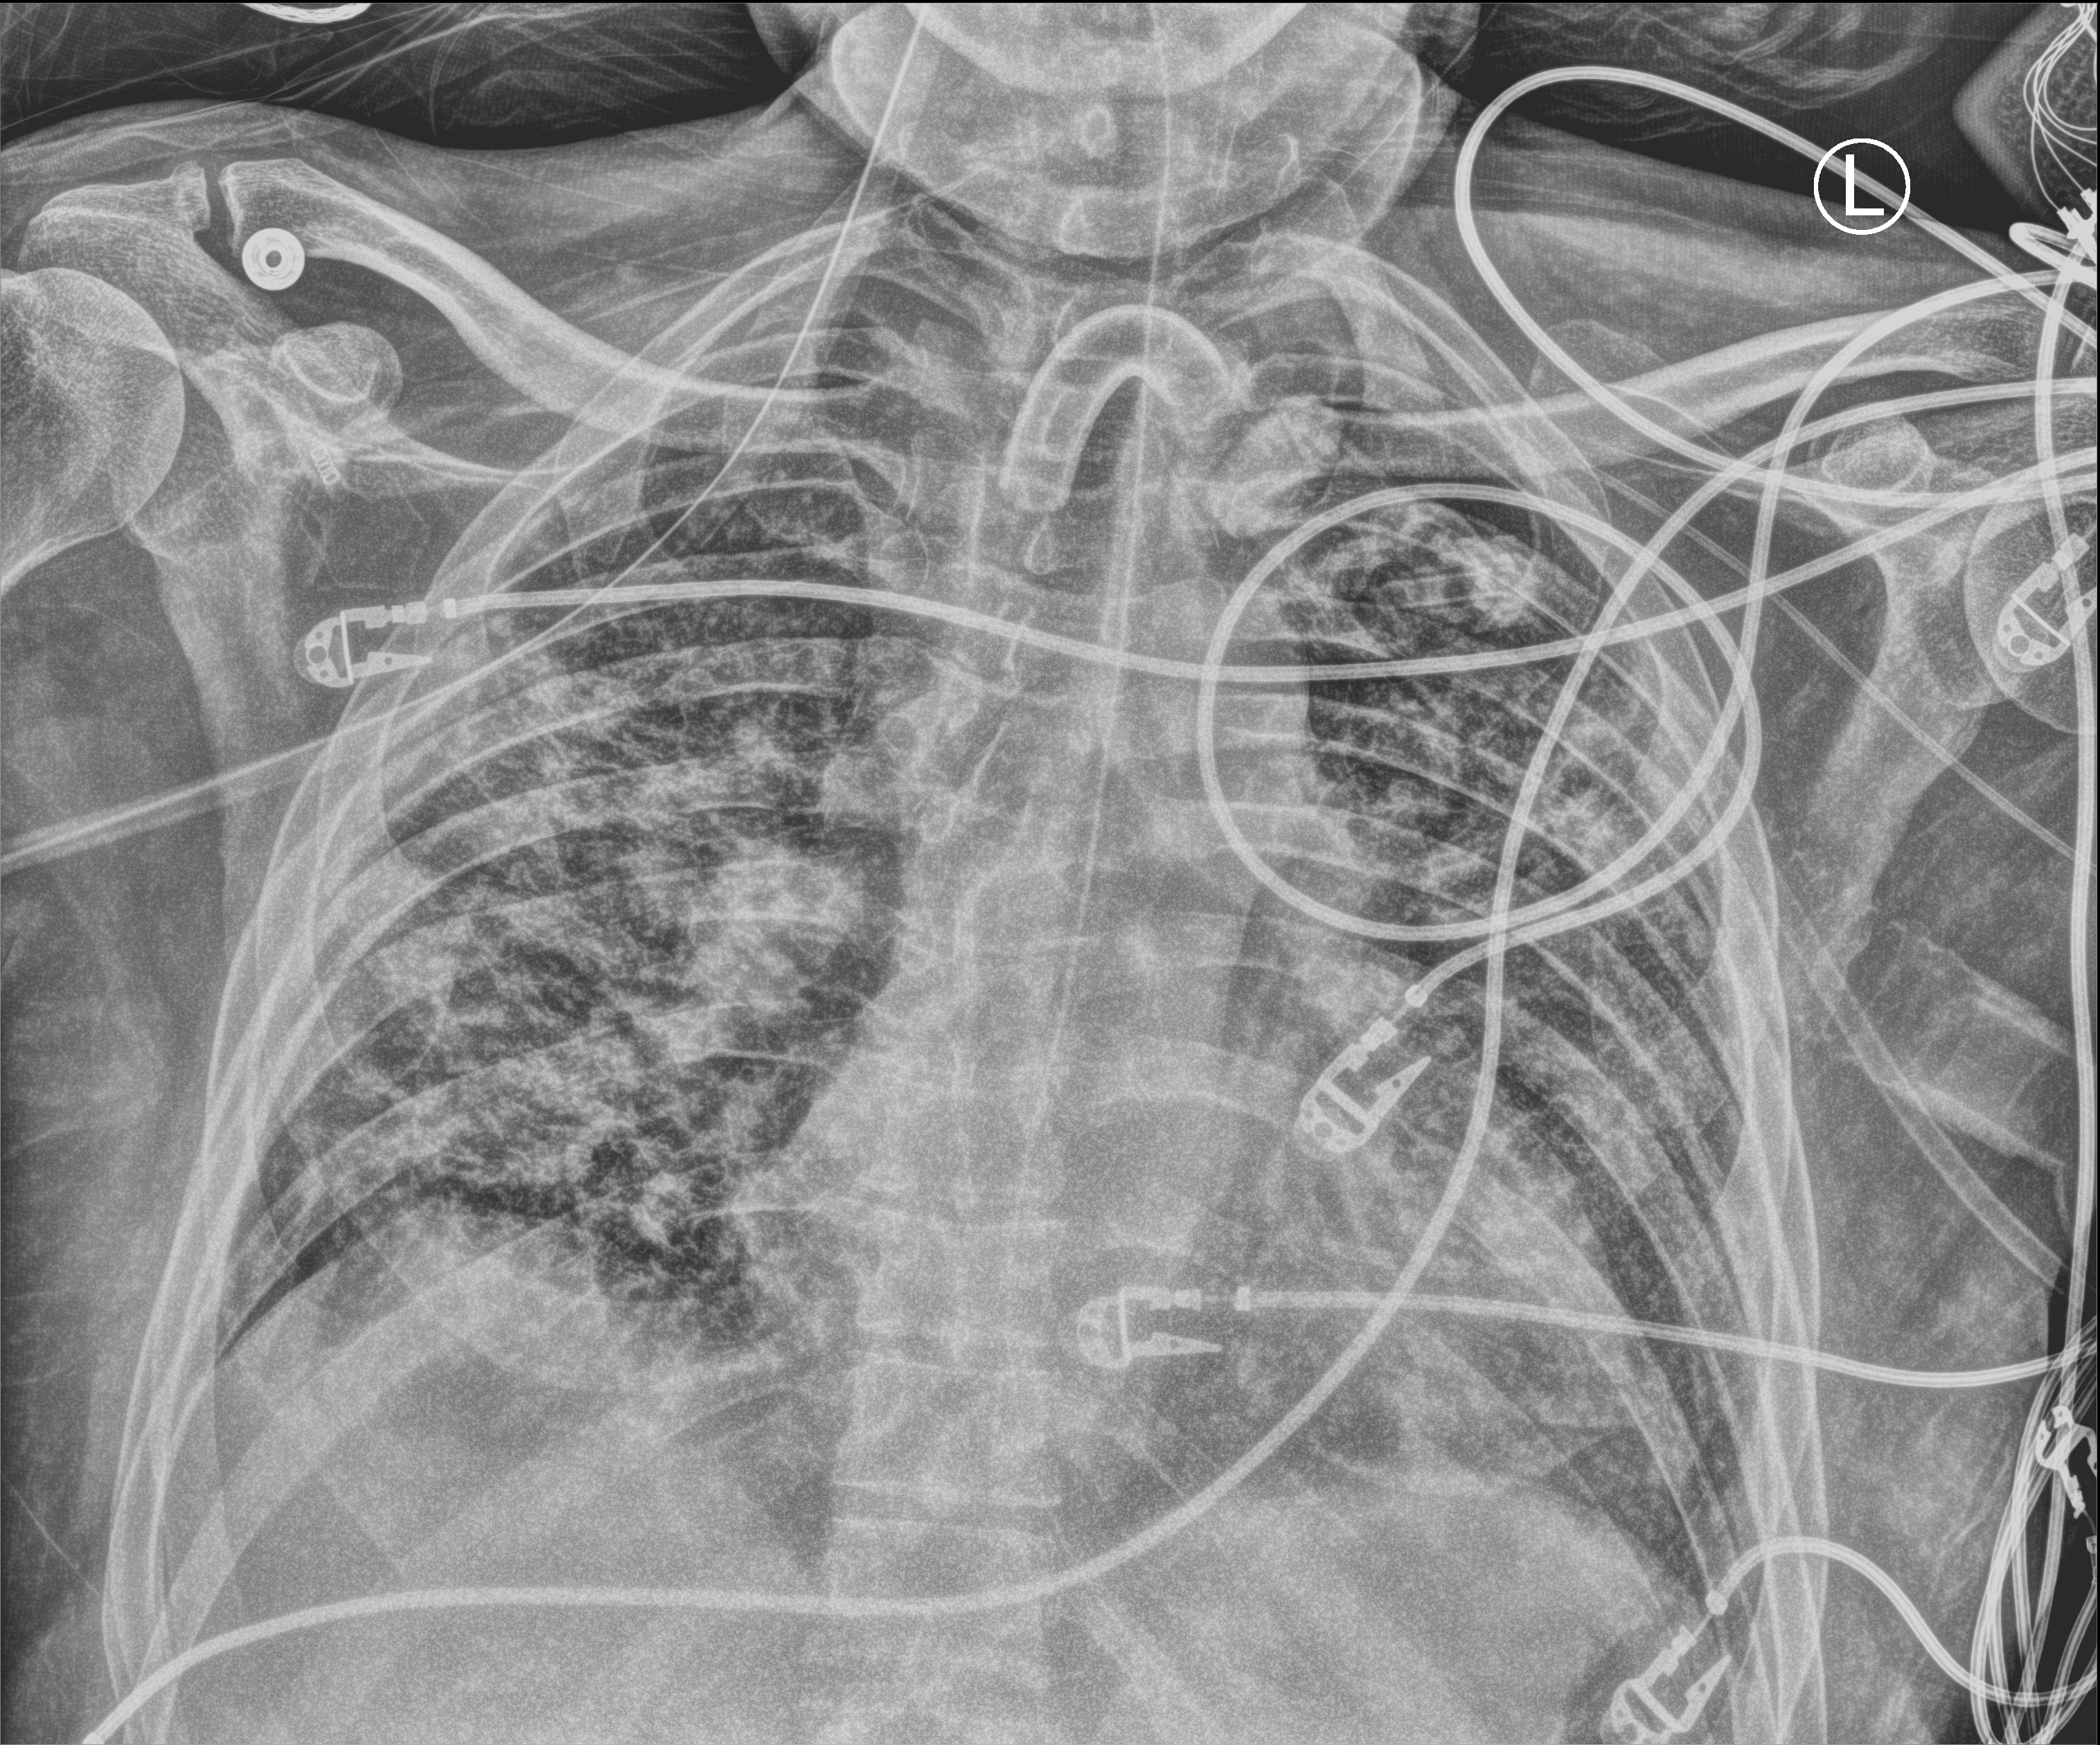
Portable chest radiograph, anteroposterior (AP) projection. Male patient hospitalised with COVID-19, age 18–59 years.
From the hospital-stay record, not from the radiograph (when in the stay this image was taken is not recorded): mechanically ventilated during this hospital stay: yes.